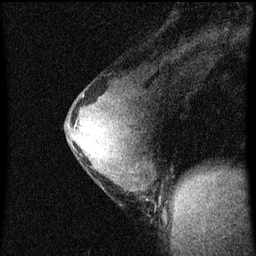
Breast MRI (dynamic contrast-enhanced), one sagittal slice. Position 36 of 60 along the scan axis. Dynamic contrast-enhanced series, image 2 of 4 at this slice position (ordered by acquisition). 1.5 T. TE 4.2 ms, TR 8 ms. 2 mm slice thickness. 256 × 256 image matrix. Female patient, age 33 years.
Outlined on this slice (semi-automatically segmented with operator editing):
- analysis volume of interest (the breast-tissue region the enhancement analysis was run in; not a lesion): box from (x=66, y=76) to (x=164, y=217) px
- tumour enhancement mask (voxels above the 70 % enhancement threshold inside the analysis volume of interest): (x=75, y=110)–(x=83, y=151)